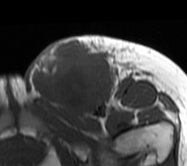
MRI of an extremity soft-tissue mass, one axial slice; position 31 of 62 along the scan axis; MR volume resampled by the dataset authors to the PET/CT grid (not the native acquisition matrix); 187 × 166 image matrix, field of view 183 × 162 mm. Female patient. Case-level facts recorded for this patient, not image findings: histological type: leiomyosarcoma; grade: high; site of the primary tumour: groin.
Structures marked on this image (expert contour drawn on MRI and transferred to this co-registered scan by the dataset authors):
- gross tumour volume including surrounding oedema: box from (x=25, y=35) to (x=140, y=120) px
- gross tumour volume (mass): (x=27, y=40)–(x=115, y=116)